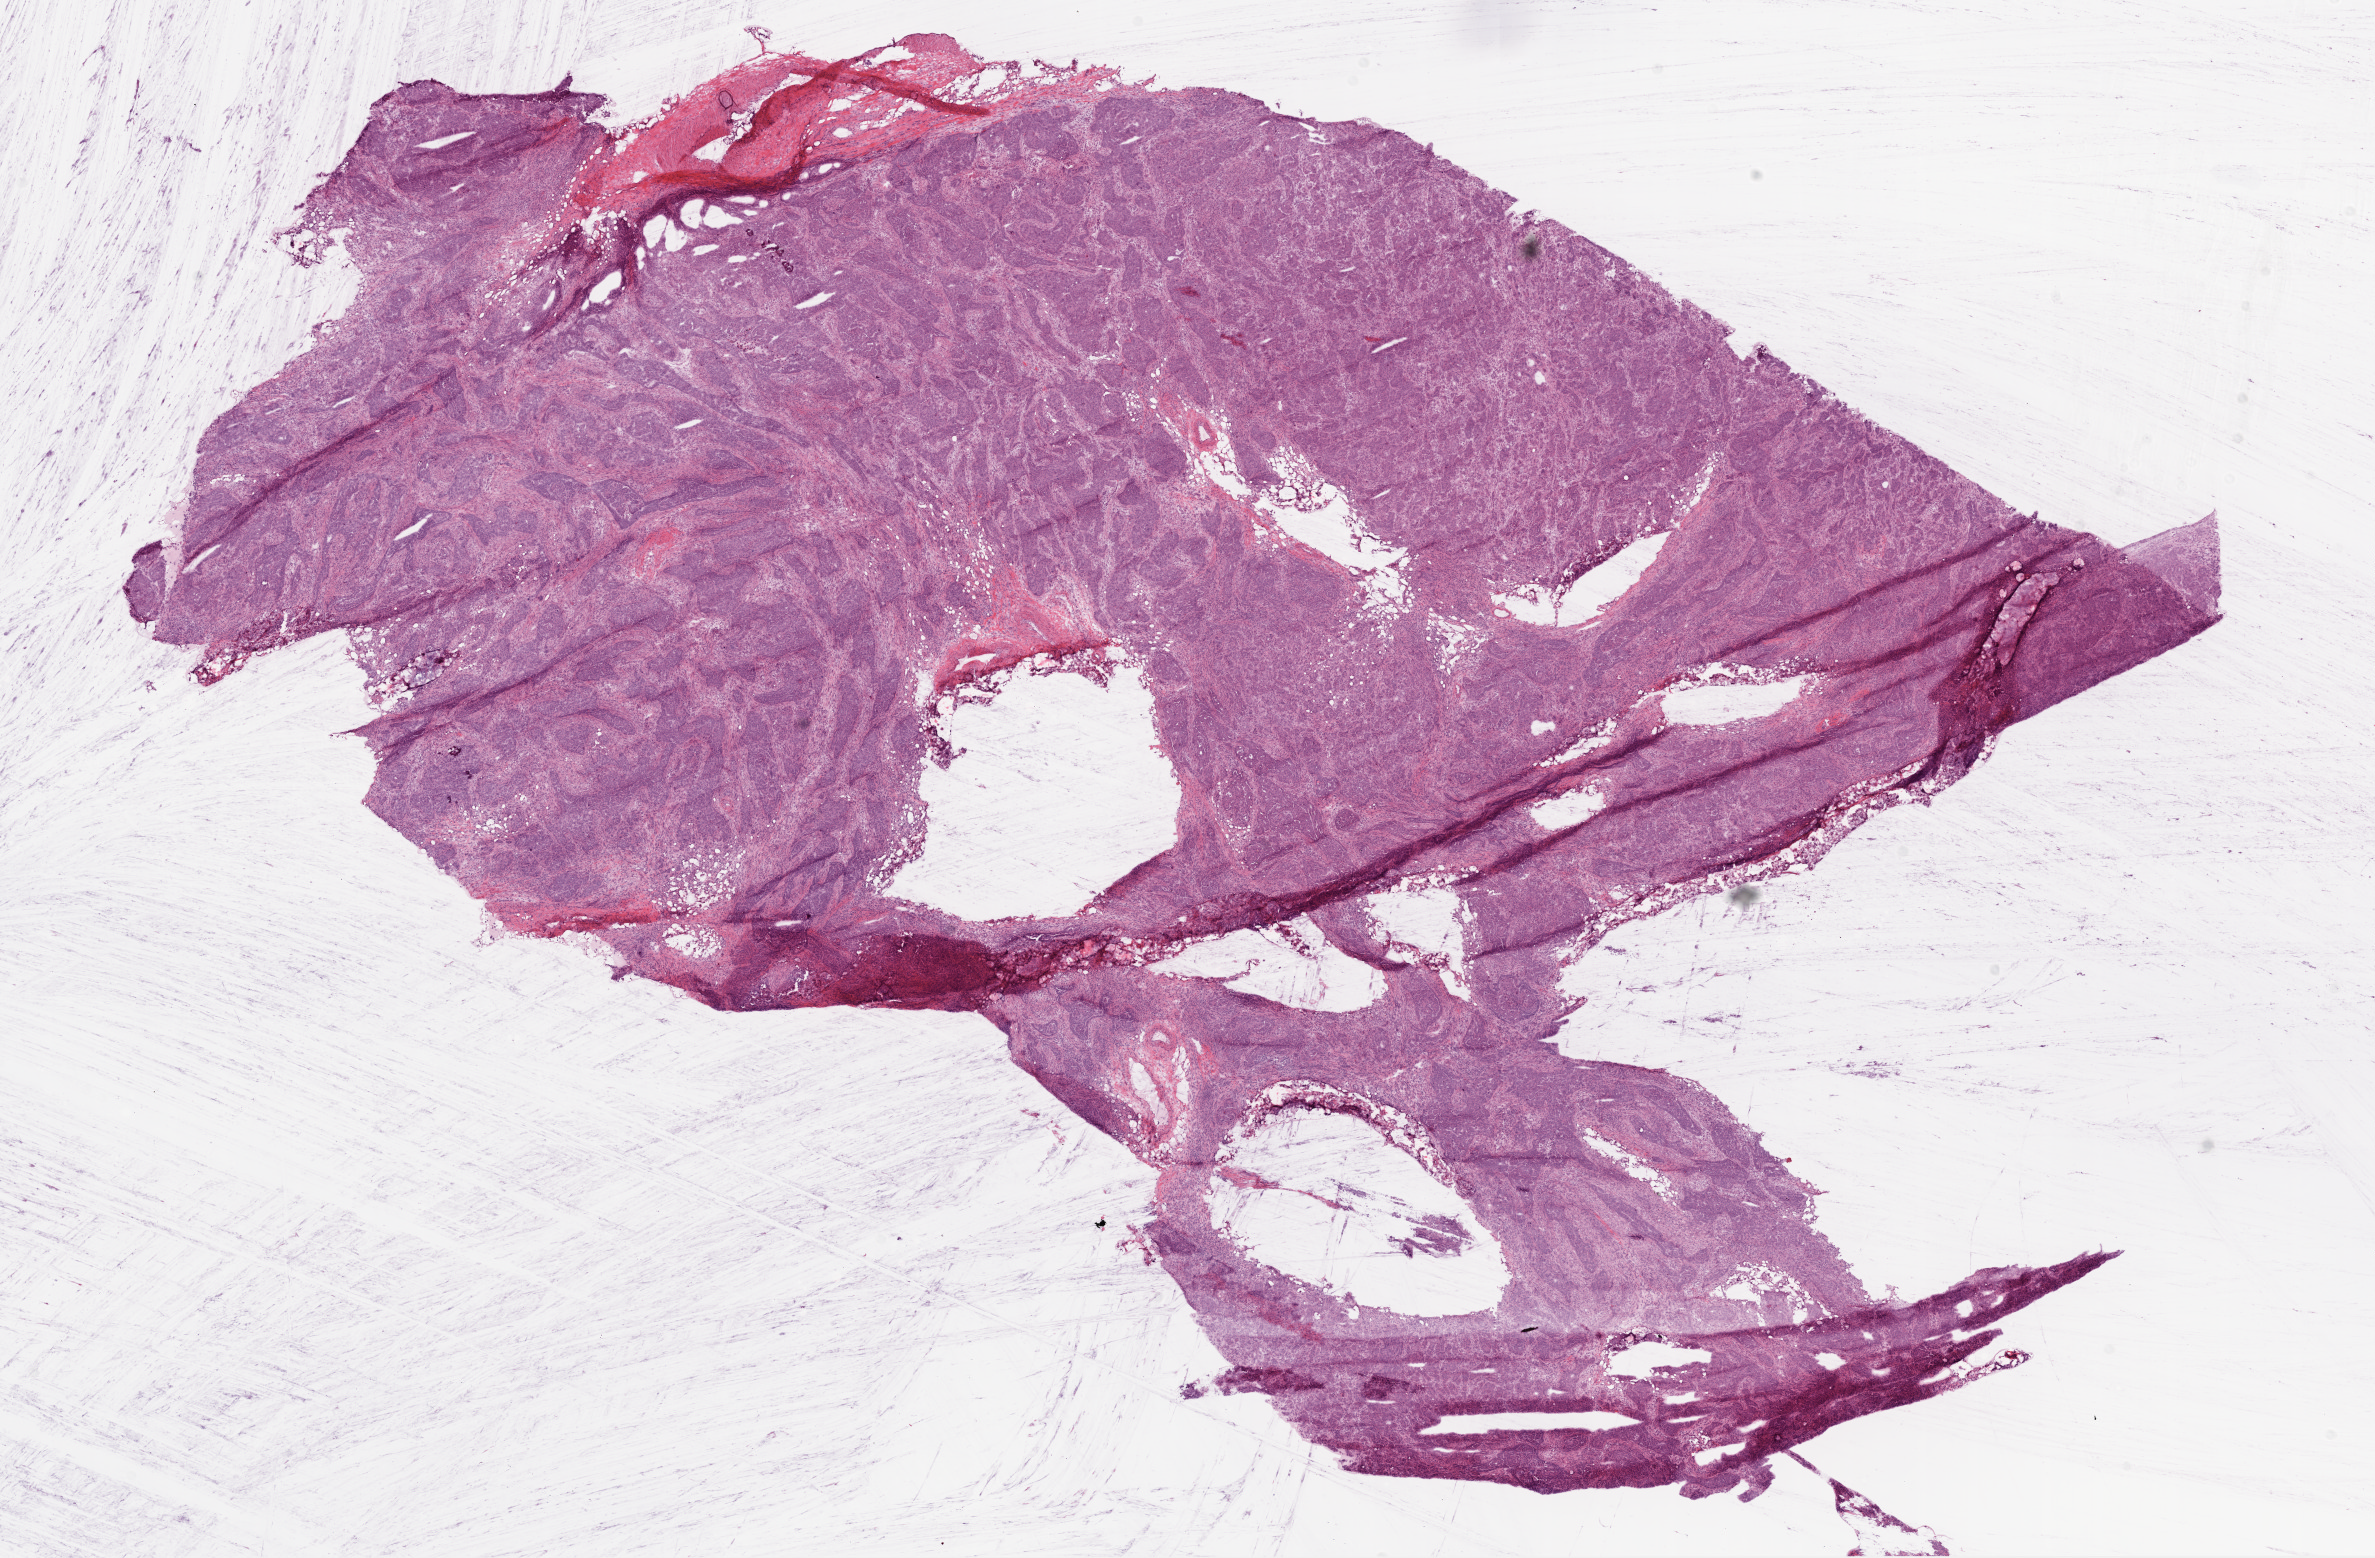
Whole-slide histology image, H&E — a low-resolution overview of the entire scanned area, about 19.1 x 12.5 mm, frozen section from the top of the tissue portion, primary tumour sample from the ovary. Female, age 76 years at initial diagnosis. Histologic grade: G3 (poorly differentiated). Pathologist review of this section (percent, as recorded): tumour cells 88%, tumour nuclei 95%, normal cells 0%, stromal cells 10%, necrosis 2%.
FIGO stage: IIIC. Diagnosis: Serous cystadenocarcinoma, NOS.